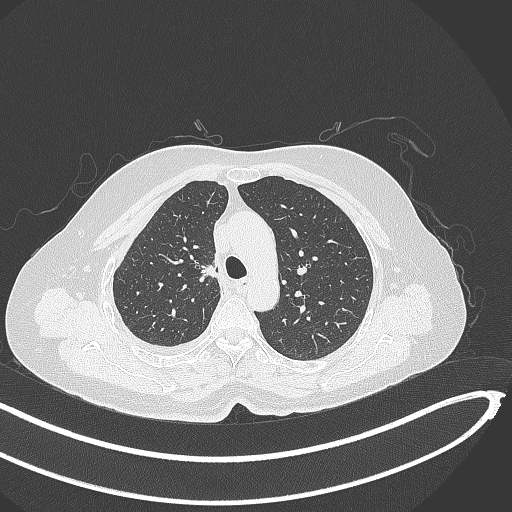
Chest CT, one axial slice; position 272 of 345 along the scan axis; reconstruction kernel B70f; 120 kVp; lung window (W 1500 / L -600 HU); 512 × 512 image matrix, field of view 400 × 400 mm. Patient: female, 64 years. From the clinical record (not read from this slice): clinical TNM (as recorded): T1b N0 M1.
Structures marked on this image (rectangle marked by the reading radiologist):
- lung tumour (recorded histology: adenocarcinoma): box from (x=194, y=254) to (x=219, y=286) px